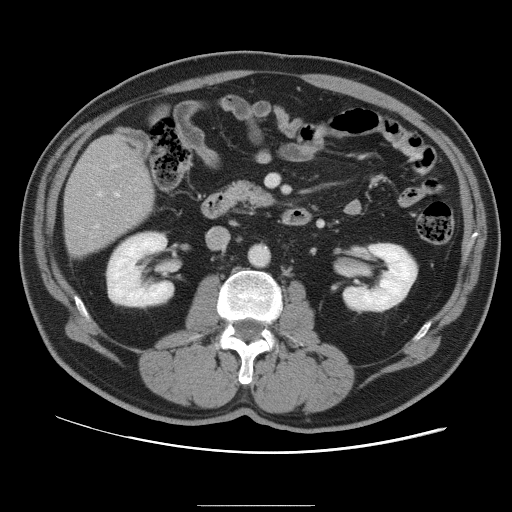
Contrast-enhanced abdominal CT, one axial slice. Slice 35 of 105 in the series (ordered by position). 120 kVp. Intravenous contrast given. Soft-tissue window (W 400 / L 40 HU). 5 mm slice thickness. 512 × 512 image matrix, field of view 399 × 399 mm. Male patient, age 64 years. From the clinical record (not read from this slice): diagnosis: colorectal cancer liver metastases, imaged before liver resection; multiple liver metastases: yes; largest metastasis: 3 cm.
Annotated regions visible in this slice (outlined manually by an expert reader):
- hepatic veins: bounding box (x1, y1, x2, y2) in pixels: (96, 193, 120, 227)
- liver: (64, 137, 153, 255)
- planned liver remnant (the part of the liver to remain after resection): (64, 137, 153, 237)
- portal vein (with intrahepatic branches): (97, 165, 117, 197)
- liver metastasis: (72, 247, 84, 253)